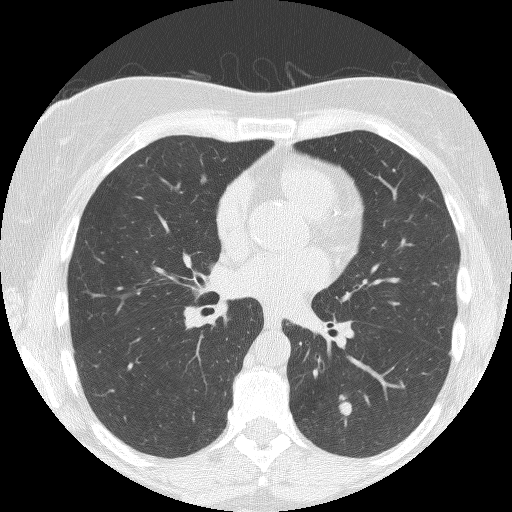
Axial slice from a low-dose chest CT screening exam, second annual screen, lung window (W 1500 / L -600 HU), 2.5 mm slice thickness, lung (sharp) reconstruction kernel (BONE), 120 kVp, slice 73 of 150 in the series. Female participant, aged 60 years at enrolment. Former smoker at enrolment.
Expert reader's lesion annotation, bounding box (x1, y1, x2, y2) in pixels: (321, 383, 360, 425). Reader record for this screening exam (exam-level; its link to the box is not recorded): non-calcified nodule or mass ≥4 mm, left lower lobe, 16 × 7 mm, smooth margins, soft tissue attenuation, pre-existing on the prior screen: no. Later outcome: lung cancer diagnosed 54 days after this screen — small cell carcinoma, NOS, left lower lobe, stage IIA (AJCC 6th edition), 12 mm at pathology.